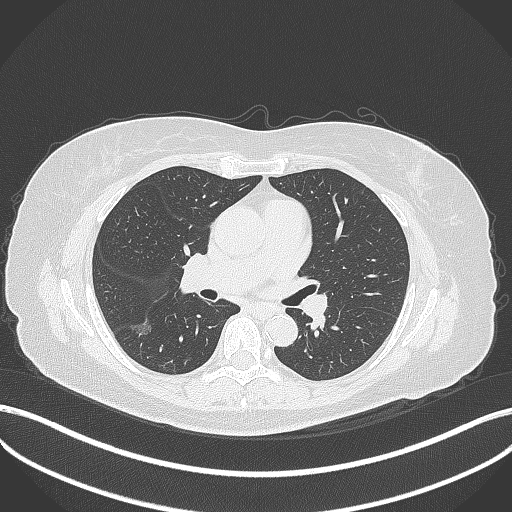
Chest CT, one axial slice; position 178 of 322 along the scan axis; reconstruction kernel B70f; lung window (W 1500 / L -600 HU); 1 mm slice thickness; 512 × 512 image matrix, field of view 400 × 400 mm. Female patient, age 64 years. From the clinical record (not read from this slice): clinical TNM (as recorded): T1c N0 M0.
Annotated regions visible in this slice (rectangle marked by the reading radiologist):
- lung tumour (recorded histology: adenocarcinoma): bounding box <129,317,156,341> (left, top, right, bottom; pixels)